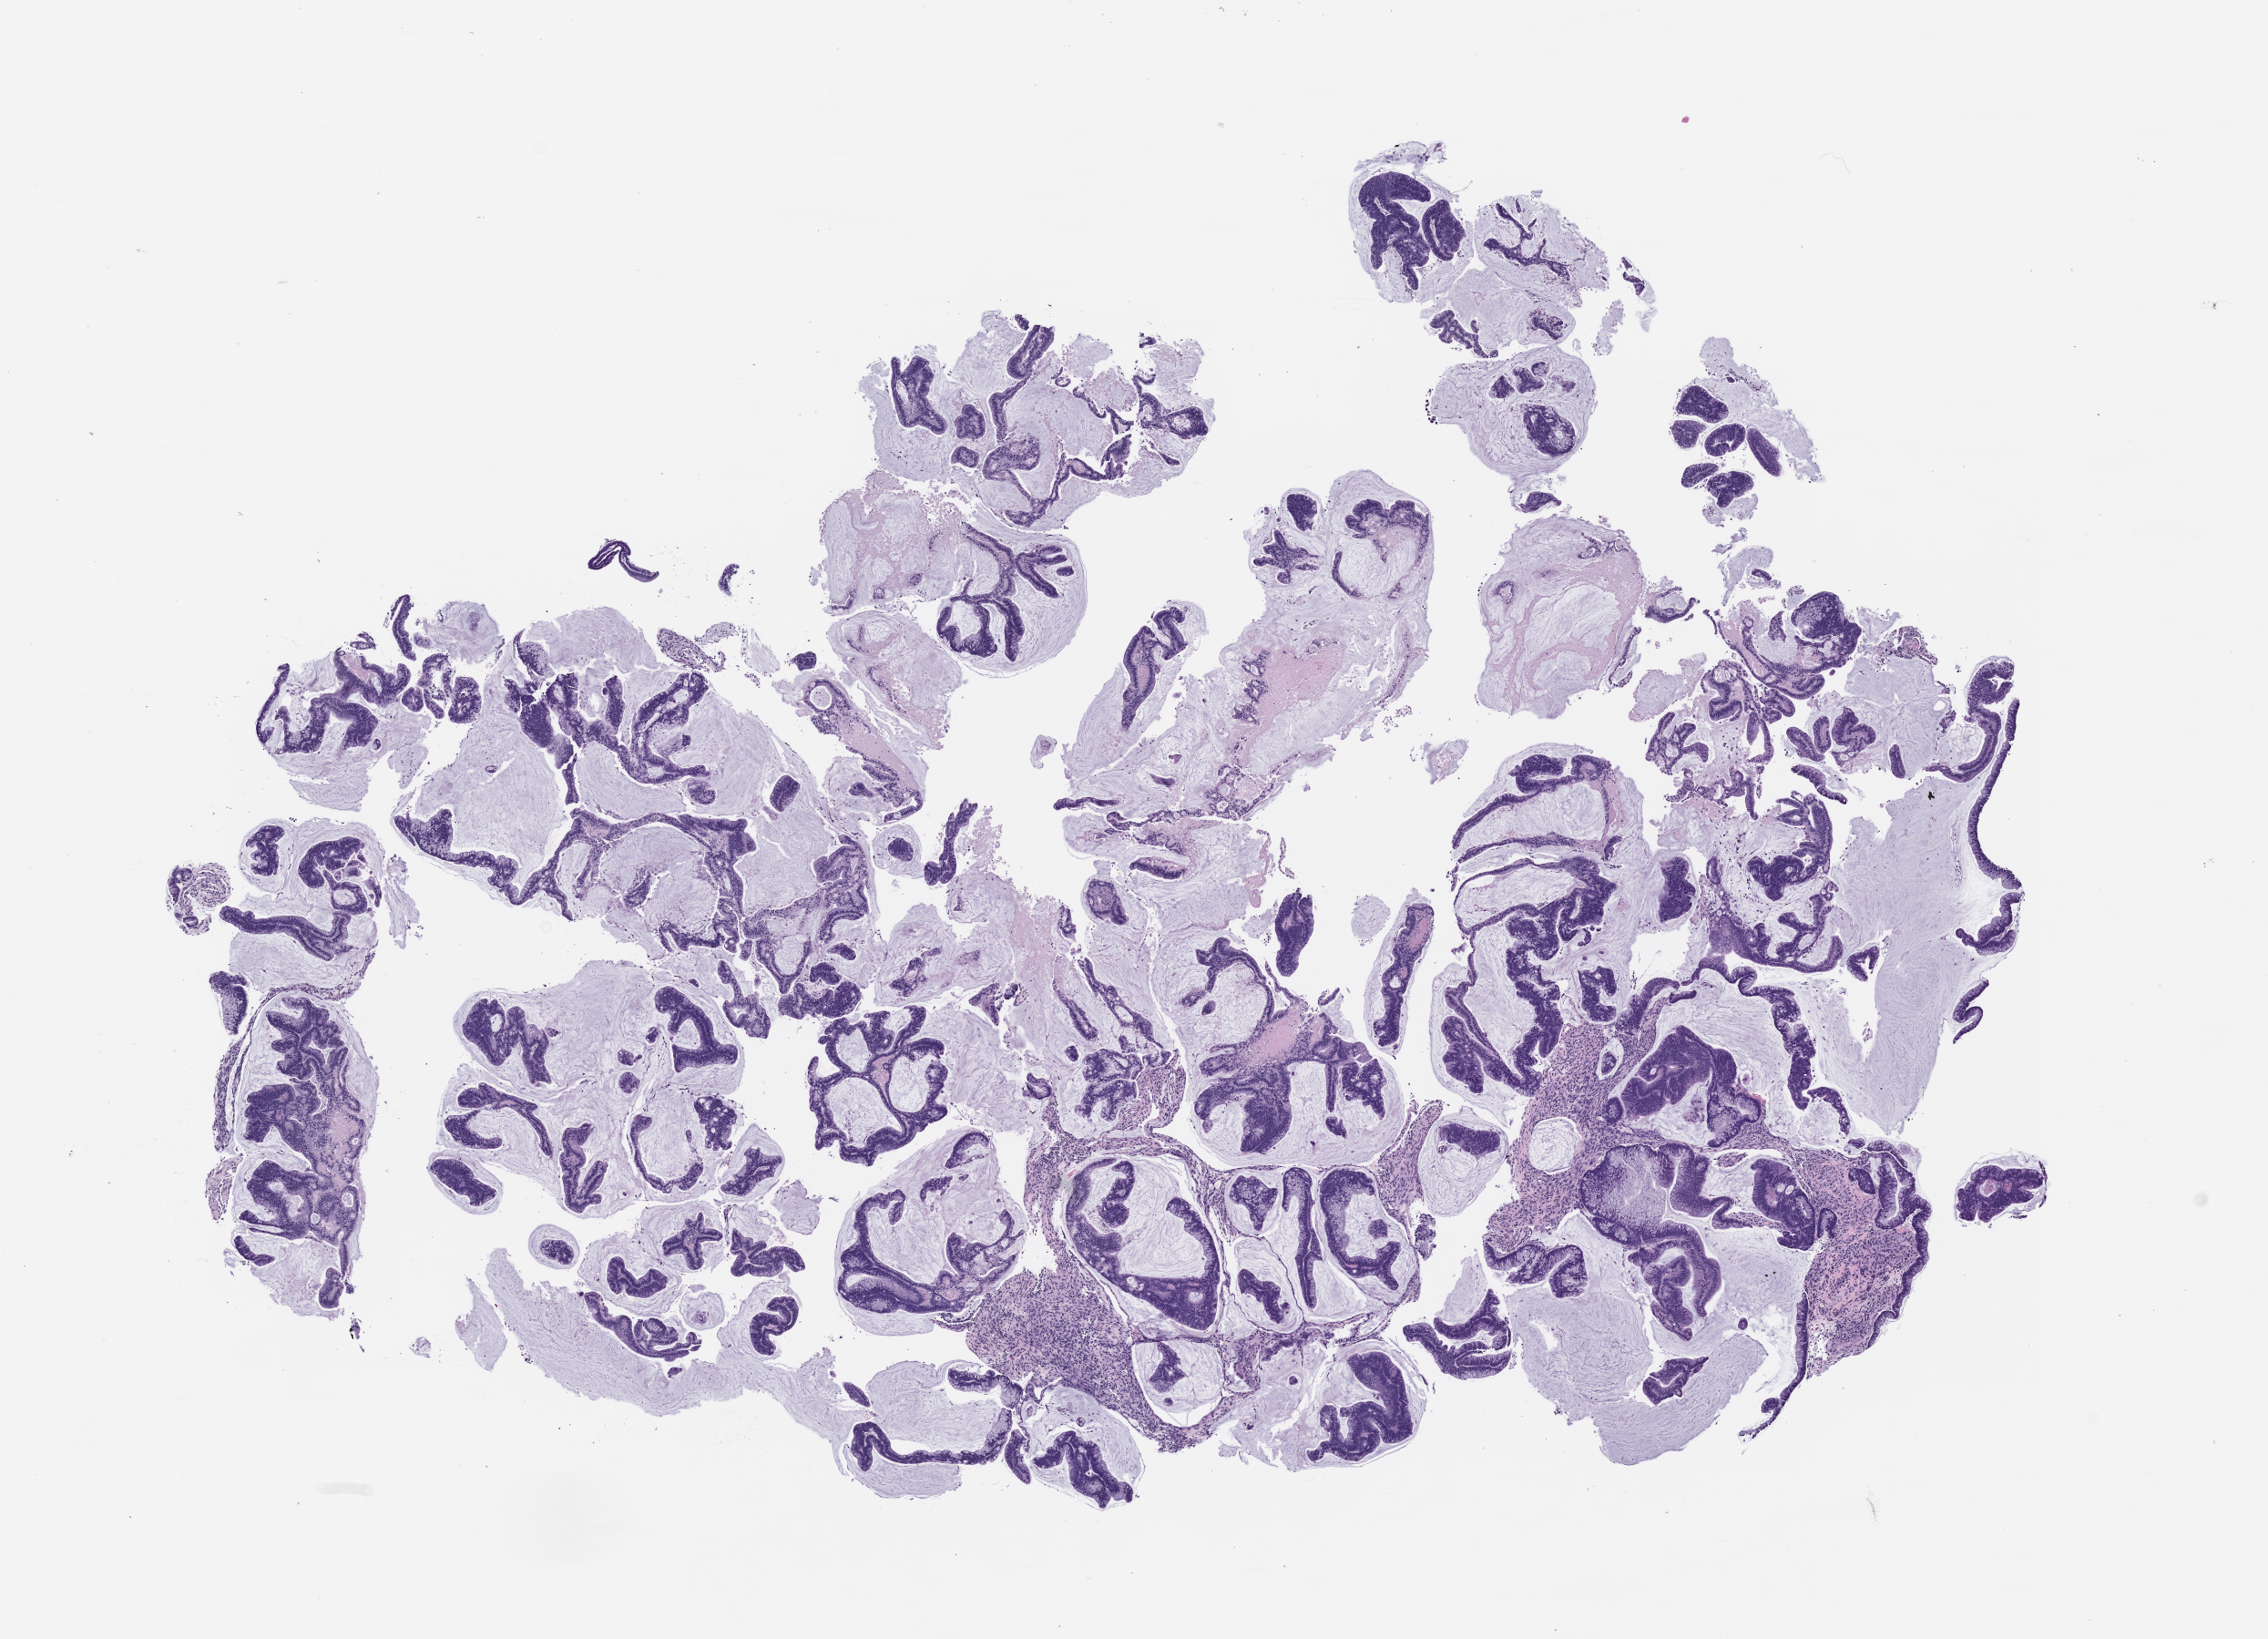
Whole-slide image, H&E: patient-derived xenograft (human tumor grown in a mouse), passage 2 — whole scanned area (about 10.0 x 7.2 mm) shown as a low-resolution overview, FFPE section, tumor site category: colon.
Originating patient diagnosis: Colon Adenocarcinoma.